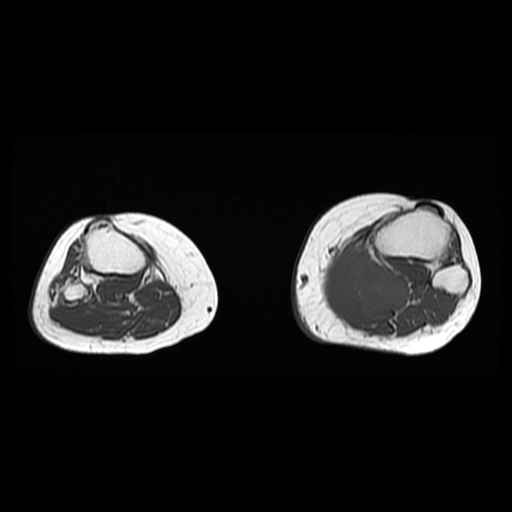
MRI of an extremity soft-tissue mass, one axial slice; slice 22 of 38 in the series (ordered by position); 6 mm slice thickness; 512 × 512 image matrix. Female patient. From the clinical record (not read from this slice): histological type: extraskeletal high grade osteogenic sarcoma; grade: high; site of the primary tumour: left calf.
Annotated regions visible in this slice (outlined manually by an expert reader):
- gross tumour volume (mass): bounding box (x1, y1, x2, y2) in pixels: (318, 242, 410, 321)